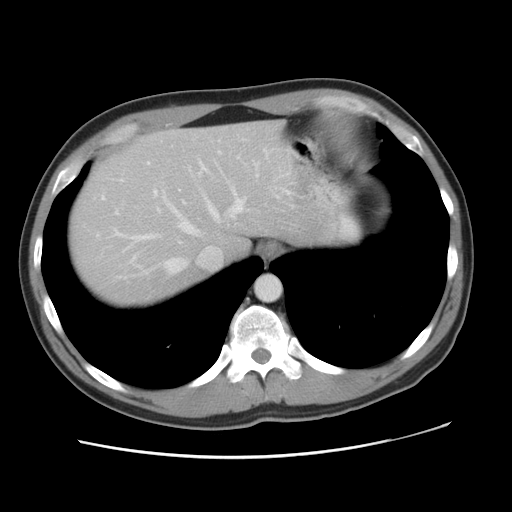
Contrast-enhanced abdominal CT, one axial slice. Position 40 of 49 along the scan axis. Intravenous contrast given. Soft-tissue window (W 400 / L 40 HU). 512 × 512 image matrix. Male patient, age 41 years. From the clinical record (not read from this slice): diagnosis: colorectal cancer liver metastases, imaged before liver resection; multiple liver metastases: yes; largest metastasis: 0.7 cm; disease in both lobes: yes.
Annotated regions visible in this slice (manually delineated by an expert):
- hepatic veins: bounding box [x1, y1, x2, y2] px = [102, 186, 246, 273]
- liver: [68, 122, 299, 306]
- planned liver remnant (the part of the liver to remain after resection): [107, 122, 300, 260]
- portal vein (with intrahepatic branches): [116, 151, 288, 260]